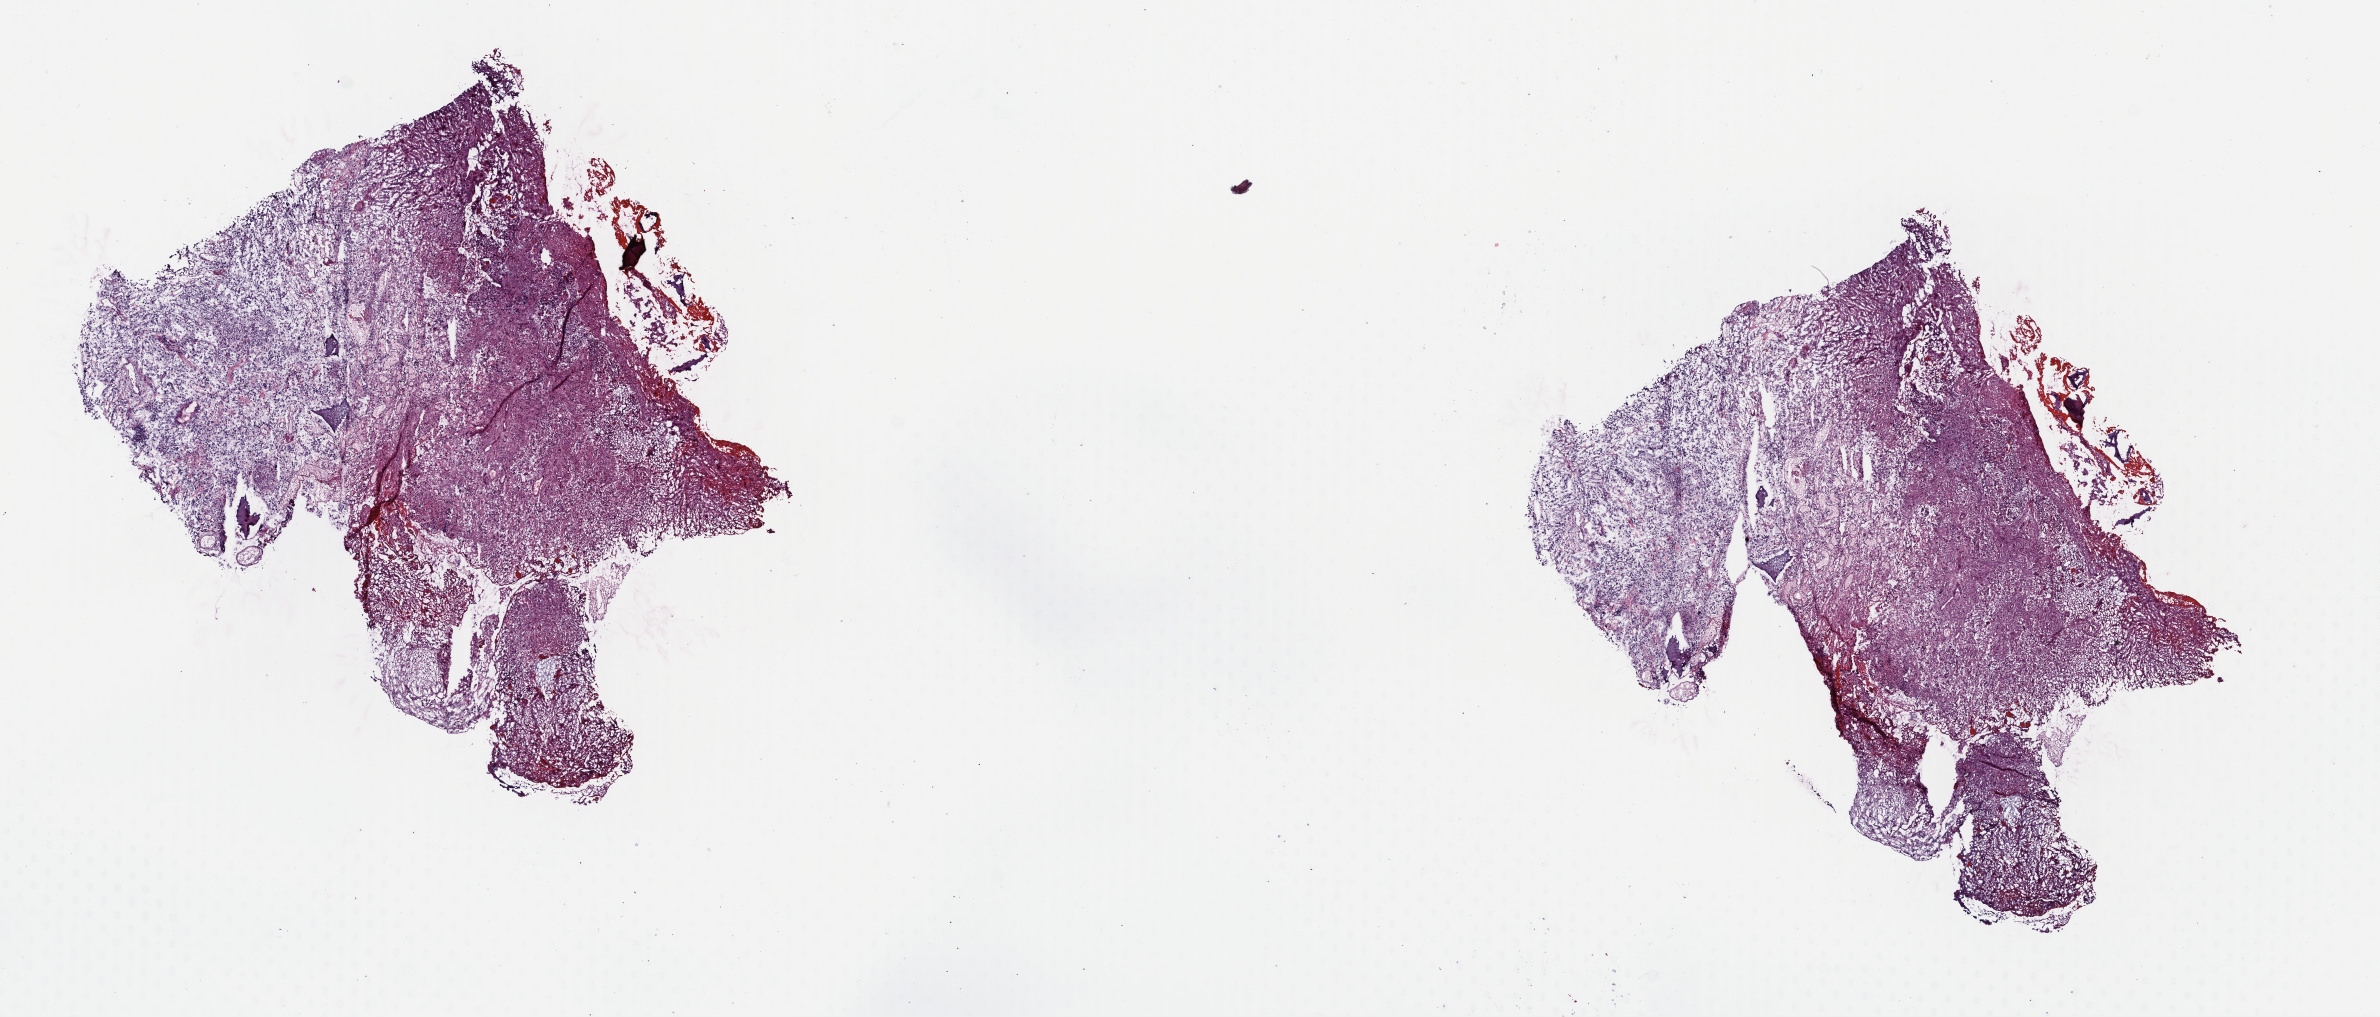
Hematoxylin and eosin (H&E) stained whole-slide image, whole scanned area (about 18.7 x 8.0 mm) shown as a low-resolution overview; frozen section from the top of the tissue portion; brain, recurrent tumour sample. Patient: male, age at initial diagnosis 23 years. Pathologist review of this section (percent, as recorded): tumour cells 70%, tumour nuclei 70%, normal cells 0%, stromal cells 30%, necrosis 0%. Infiltration values recorded for this section: lymphocyte infiltration 5%, monocyte infiltration 0%, neutrophil infiltration 0%.
This section: recurrent tumour. Patient diagnosis: Astrocytoma, anaplastic (cerebrum).